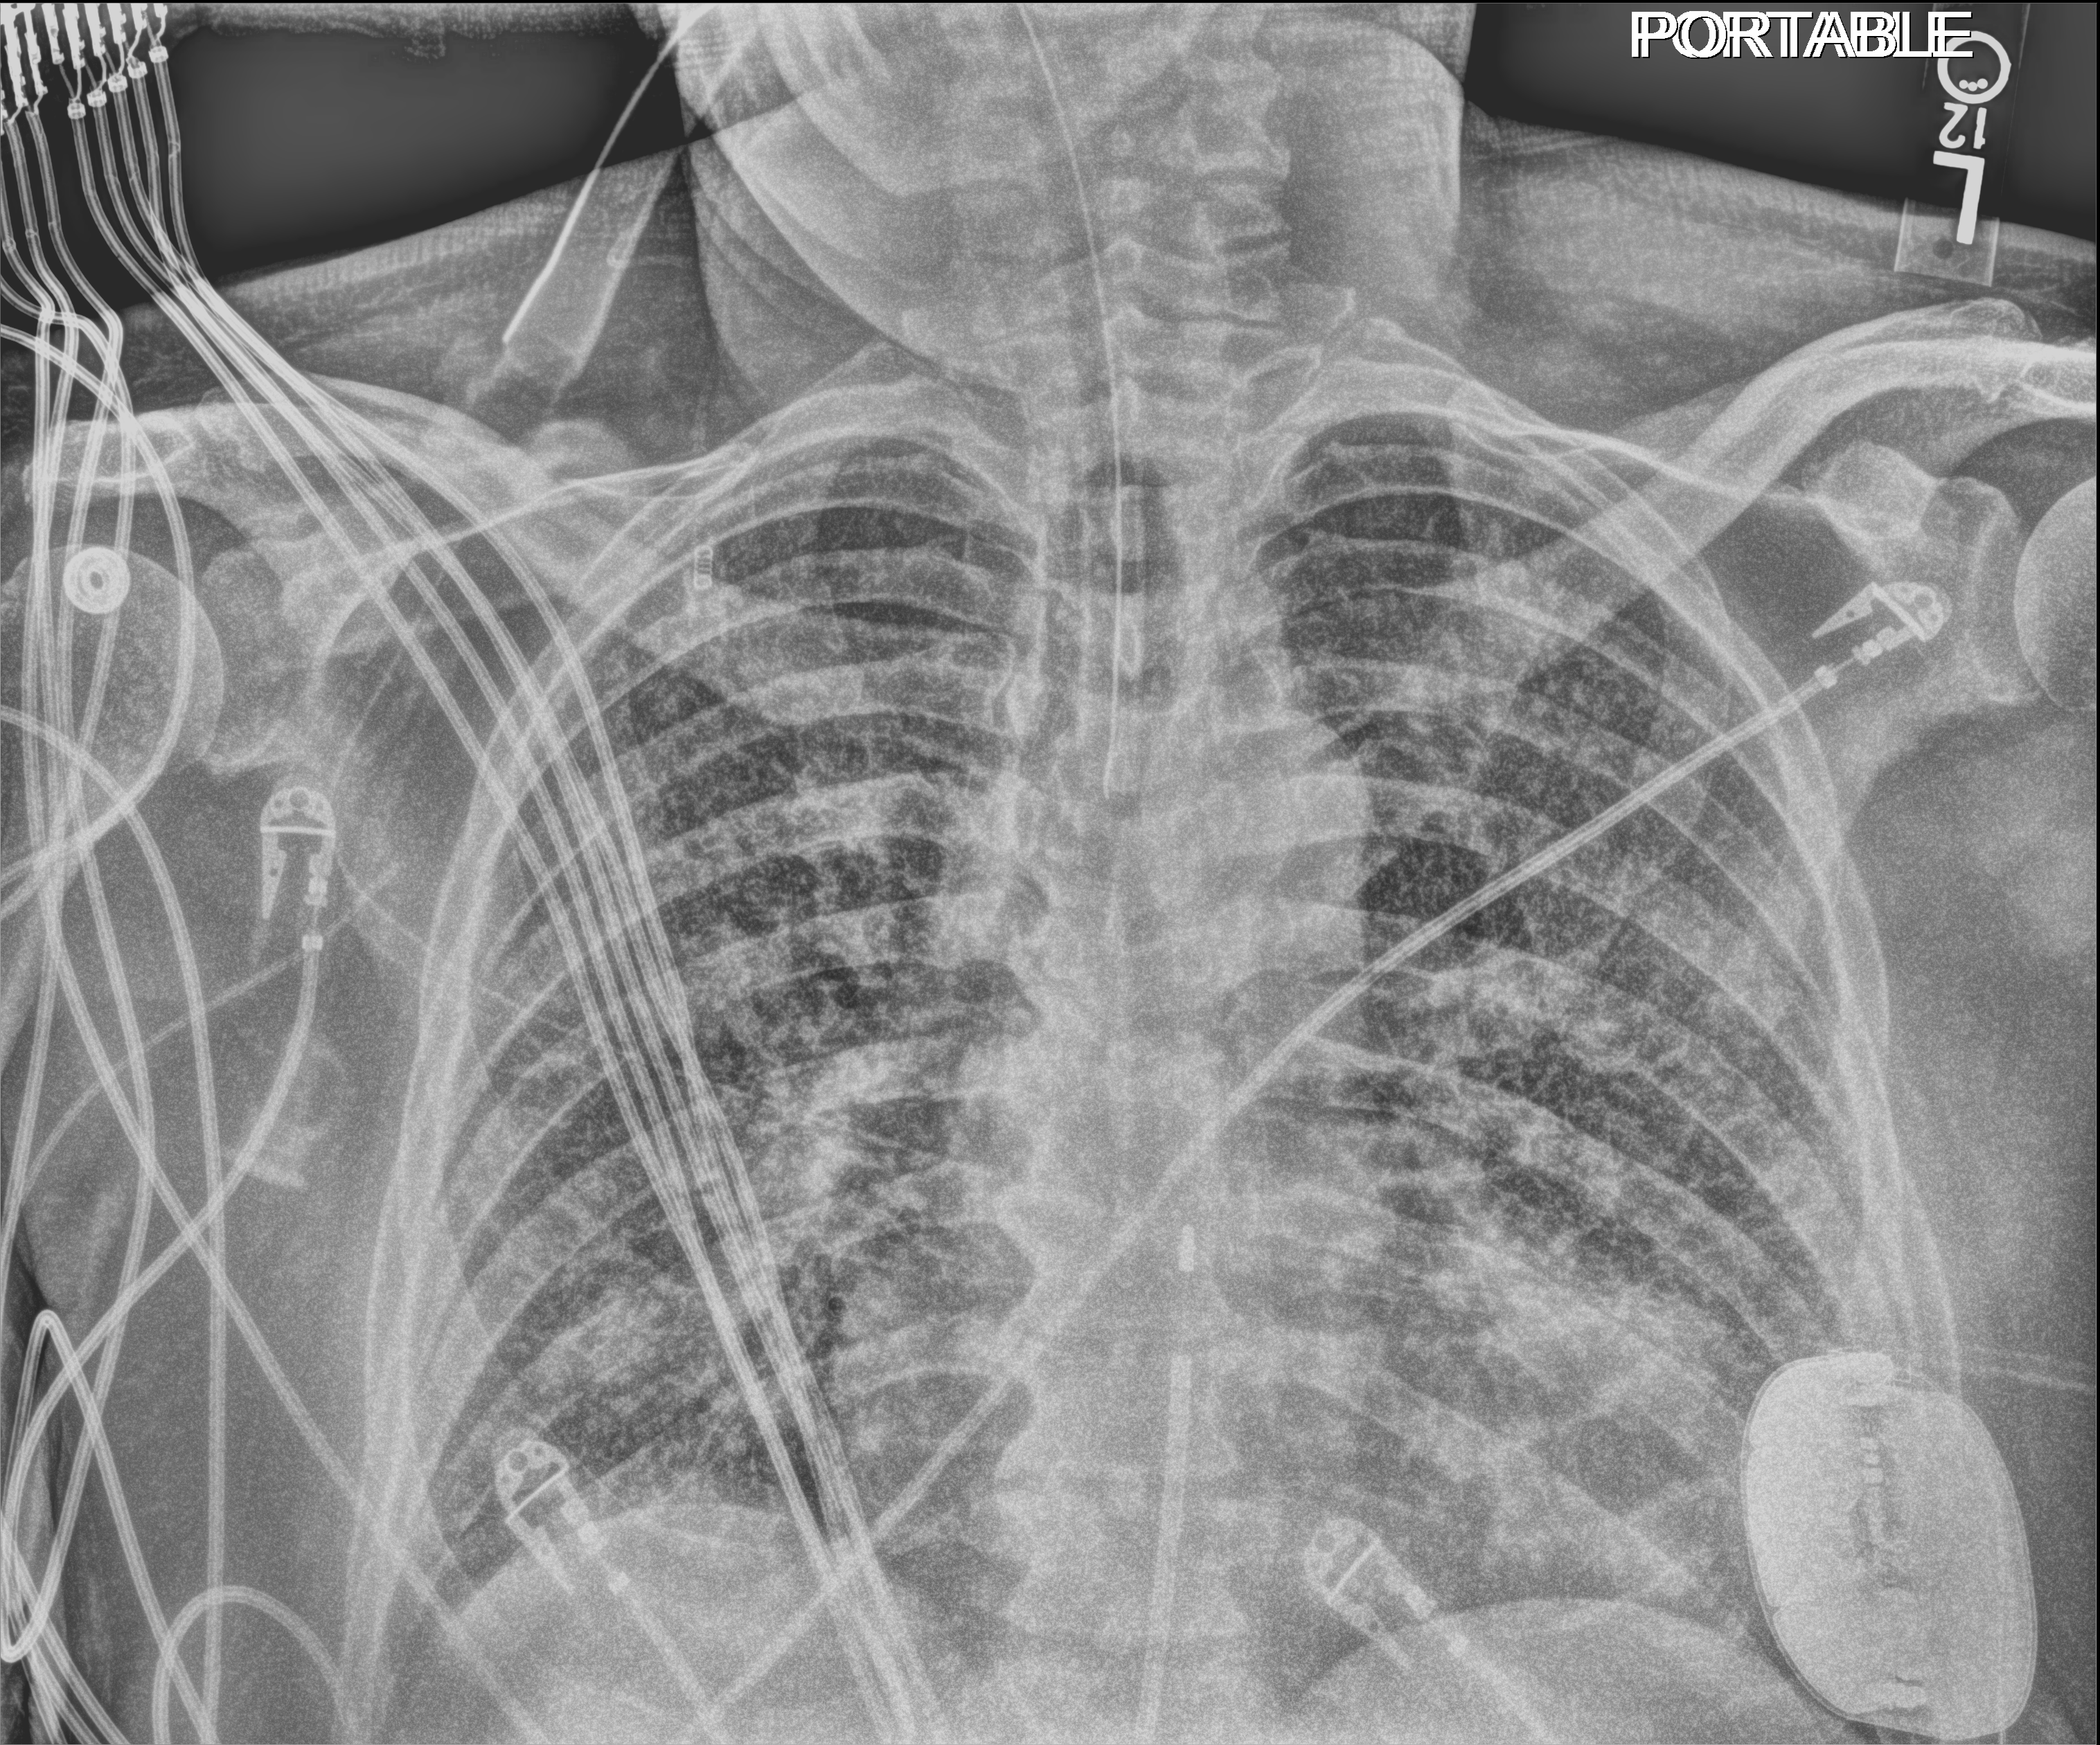
Portable chest radiograph. Male patient hospitalised with COVID-19, age 60–74 years.
Hospital-stay facts (about this admission, not read from this image; timing relative to this image not recorded): other chronic lung disease (admission record): no; mechanically ventilated during this hospital stay: yes; admitted to intensive care during this hospital stay: yes.